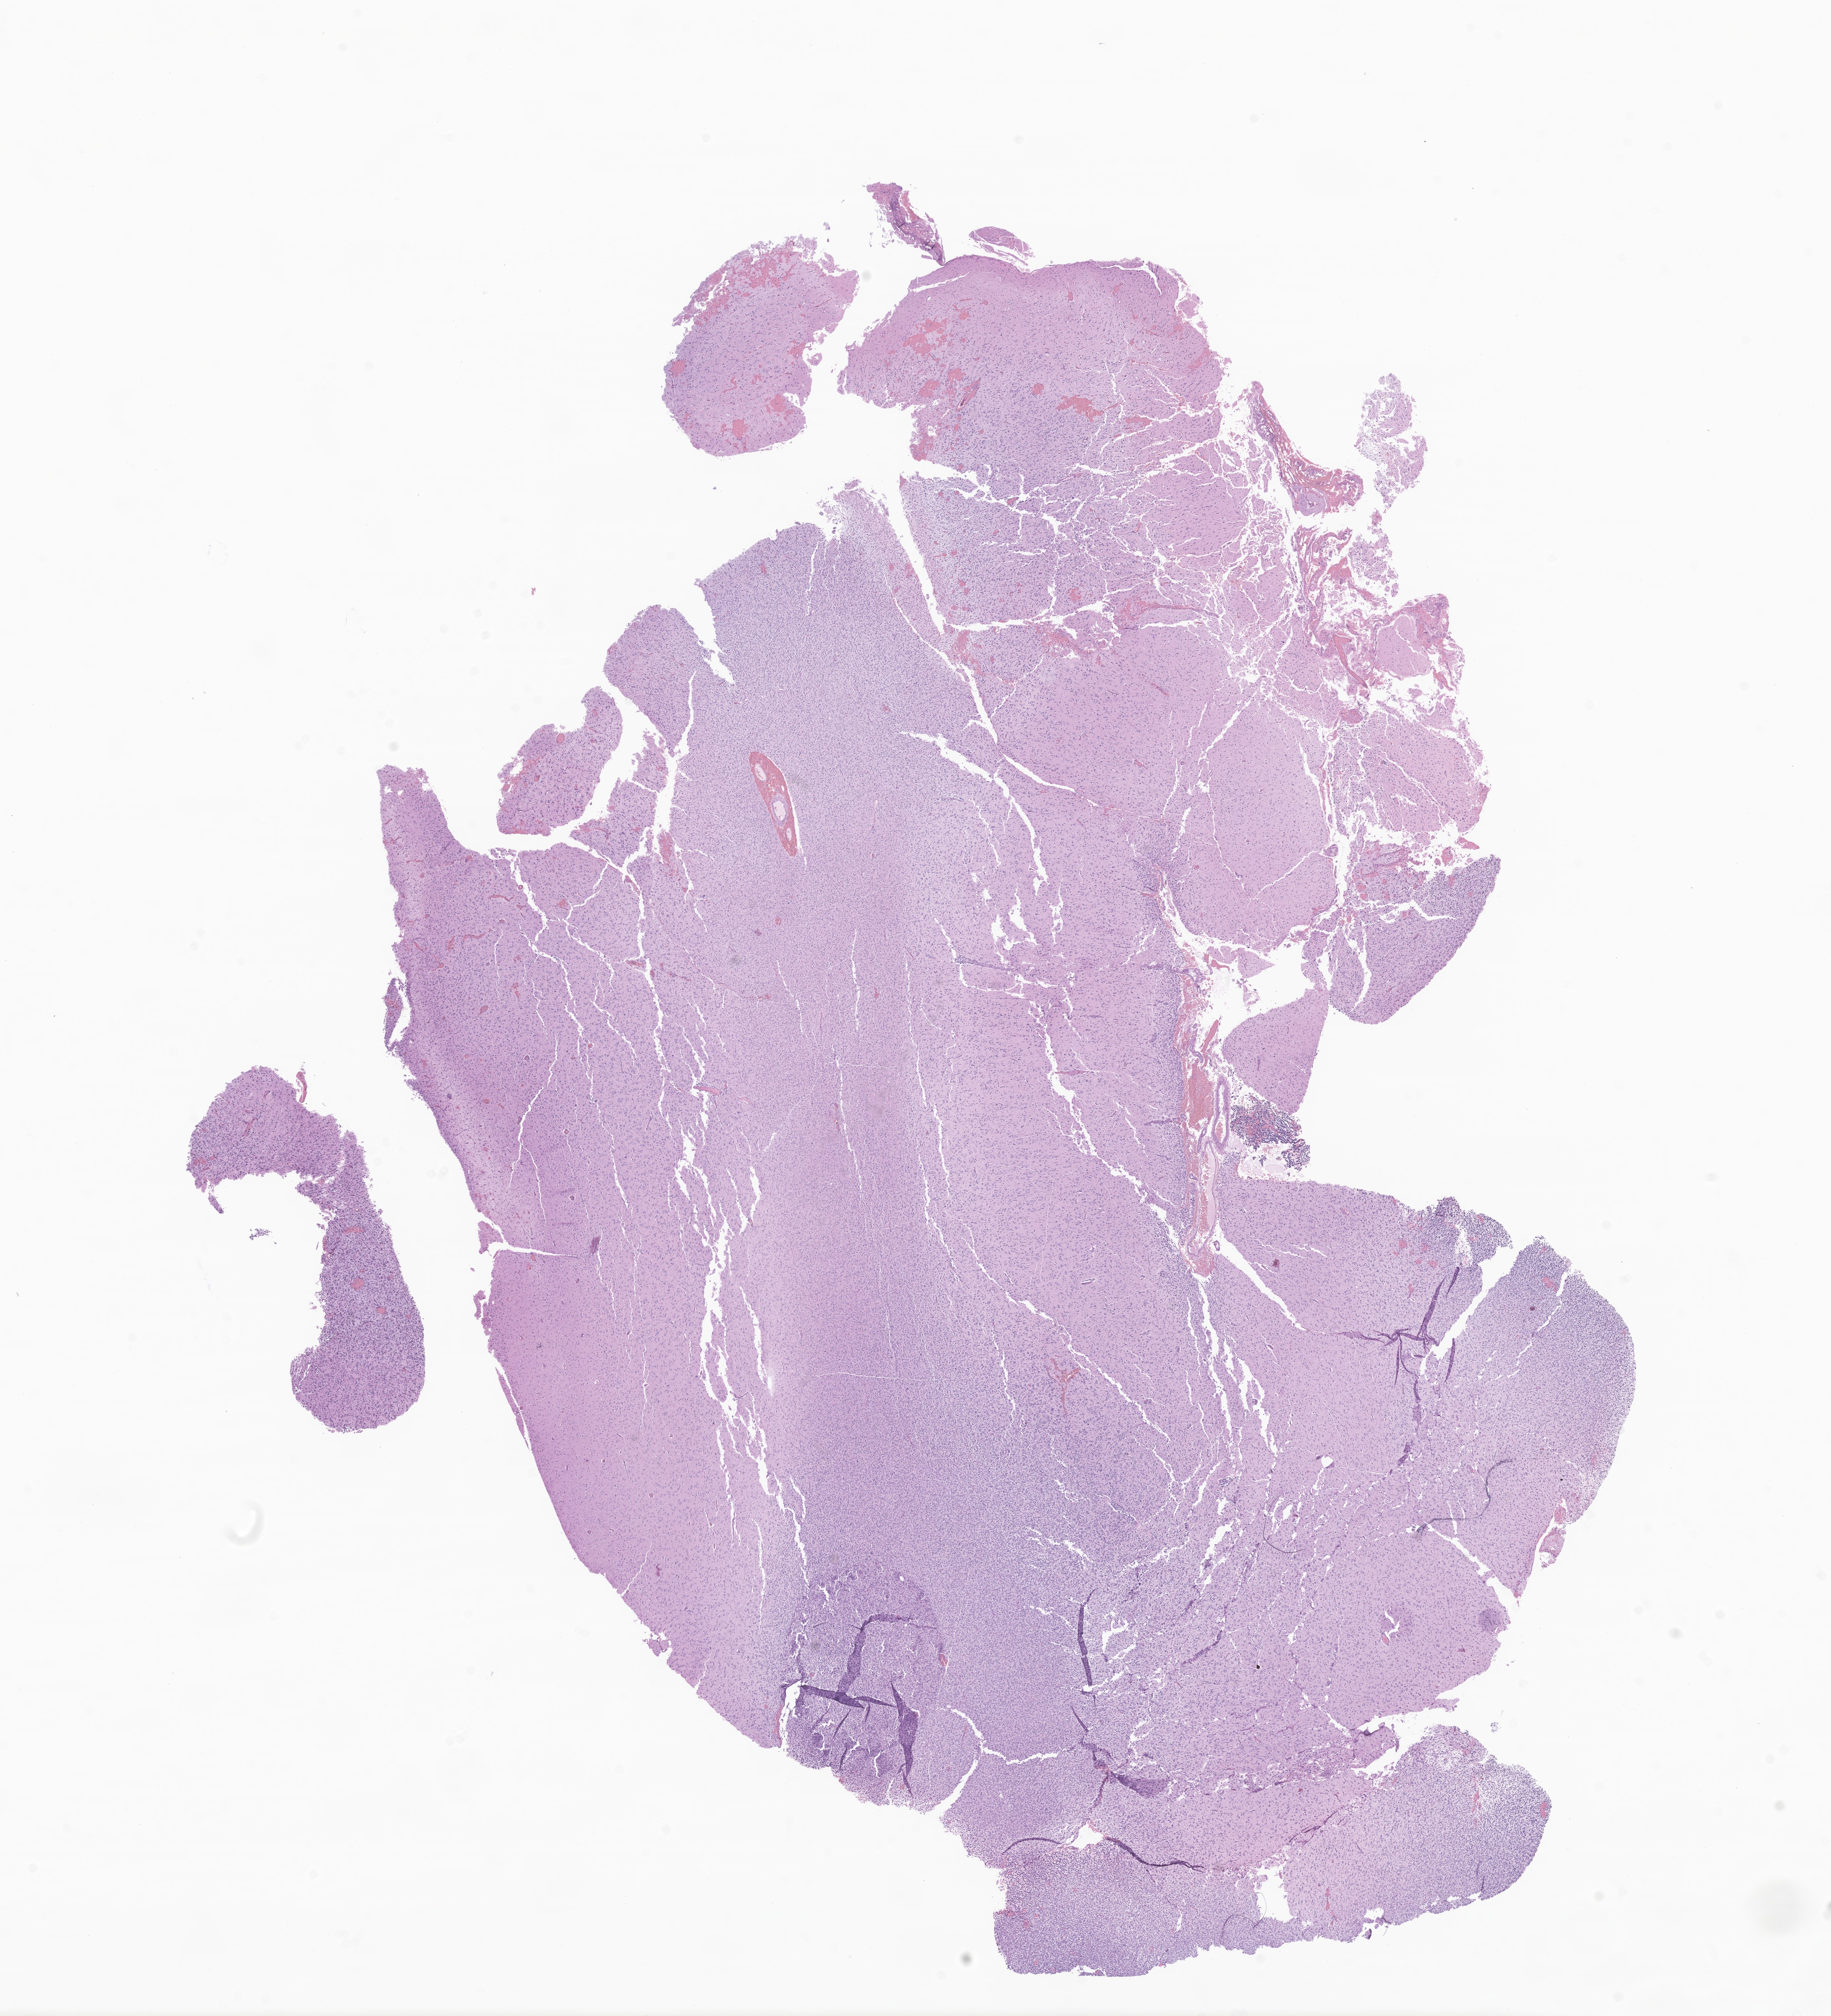
Digitized haematoxylin and eosin-stained section of tumor tissue from the brain, whole scanned area (about 17.8 x 19.6 mm) shown as a low-resolution overview; formalin-fixed, paraffin-embedded (FFPE) tissue. Patient male; age 62 months (5 years 2 months).
* recorded diagnosis: Glioma, malignant